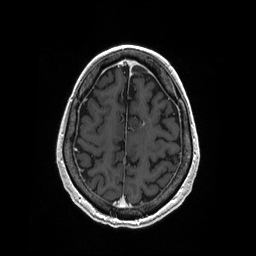
Brain MRI from a brain-tumour surgery series, one axial slice. Slice 60 of 208 in the series (ordered by position). T1-weighted post-contrast. 1 mm slice thickness. 256 × 256 image matrix, field of view 256 × 256 mm. Case-level facts recorded for this patient, not image findings: histopathology: Primary diffuse large B-cell lymphoma; tumour location: Left Corpus Callosum (Frontal).
Annotated regions visible in this slice (outlined manually by an expert reader):
- tumour: bounding box (x1, y1, x2, y2) in pixels: (142, 120, 146, 127)